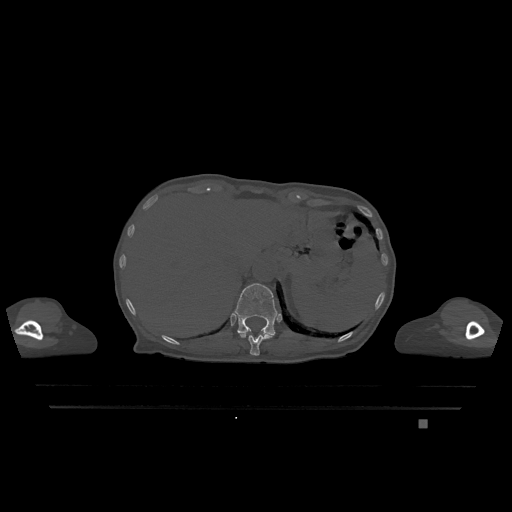
CT including the spine, one axial slice. Slice 554 of 1317 in the series (ordered by position). Bone window (W 1800 / L 400 HU). 512 × 512 image matrix. Female patient, age 74 years. From the clinical record (not read from this slice): primary cancer: lung; vertebrae with lytic lesions (as recorded): T1, T4, T5, T6, L4, L5.
Annotated regions visible in this slice (semi-automatic segmentation, software-assisted and operator-edited):
- T11 vertebra: bounding box (x1, y1, x2, y2) in pixels: (239, 333, 273, 356)
- T12 vertebra: (234, 283, 278, 336)